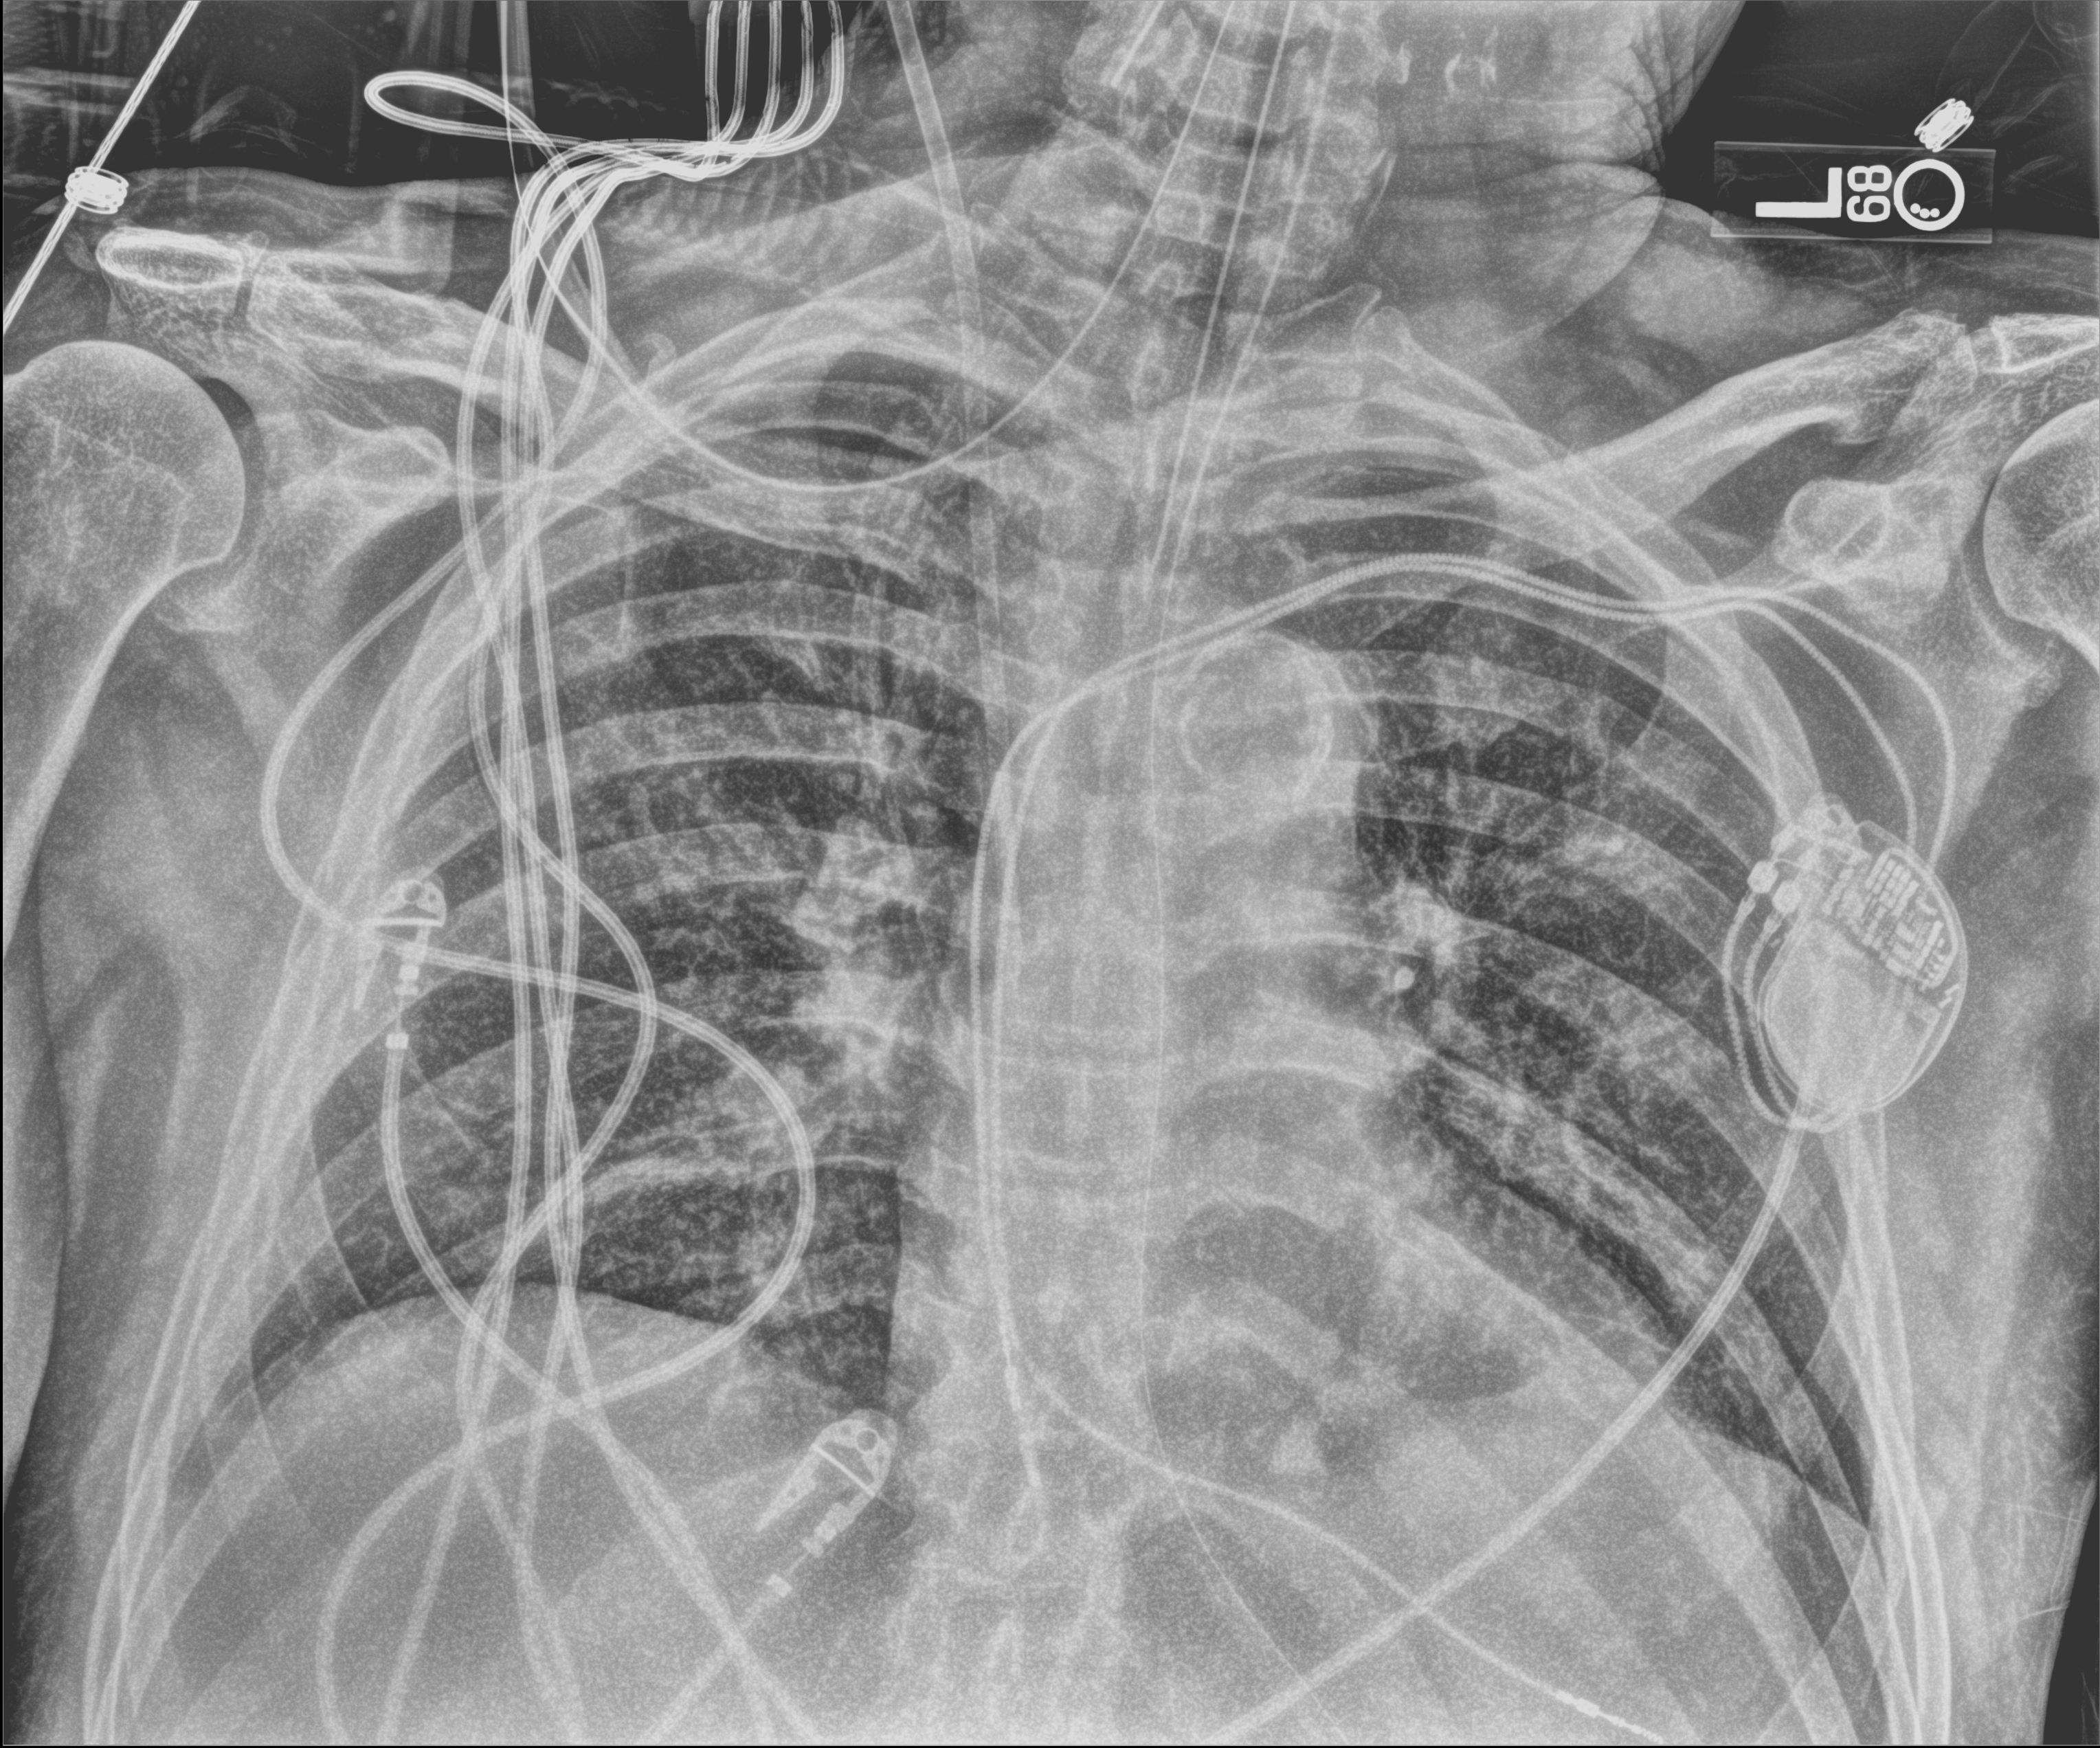
Chest X-ray (portable). Patient hospitalised with COVID-19; male, aged 60–74 years.
Hospital-stay facts (about this admission, not read from this image; timing relative to this image not recorded):
- admitted to intensive care during this hospital stay: yes
- mechanically ventilated during this hospital stay: yes